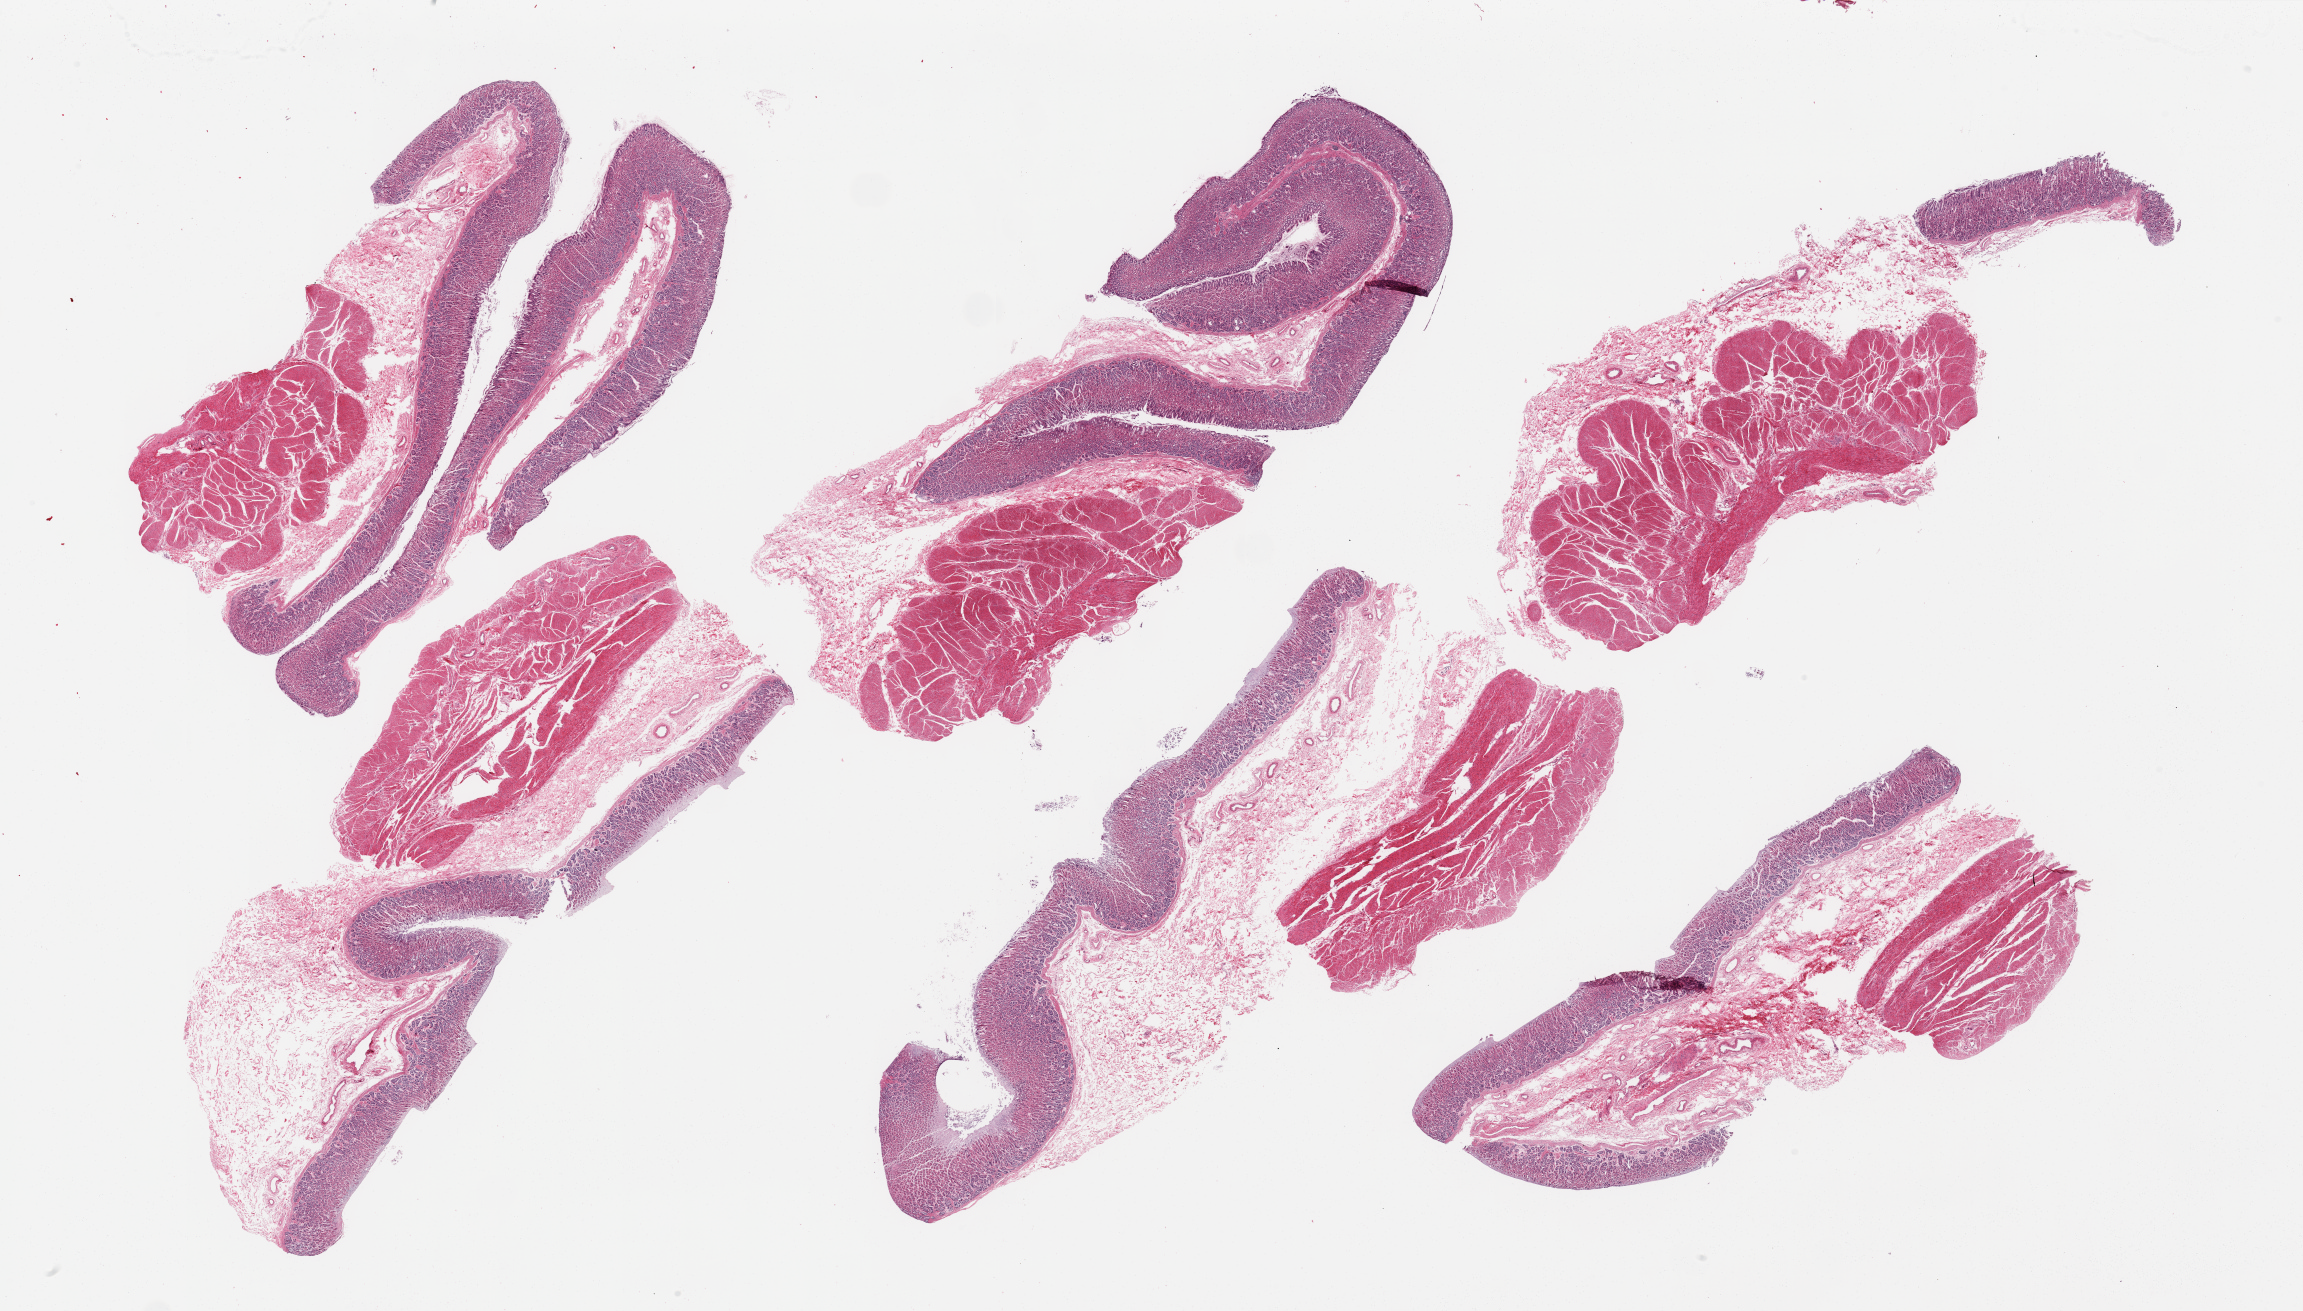
Whole-slide image, haematoxylin and eosin stain, brightfield — shown as a low-resolution overview of the whole scanned area (about 36.4 x 20.7 mm, from a 20x scan); PAXgene-fixed, paraffin-embedded tissue; target tissue: stomach; donor tissue sample. Donor sex: female.
Pathologist's review note for this sample: 6 pieces; mucosa/submucosa/muscularis; mild to moderate autolysis.